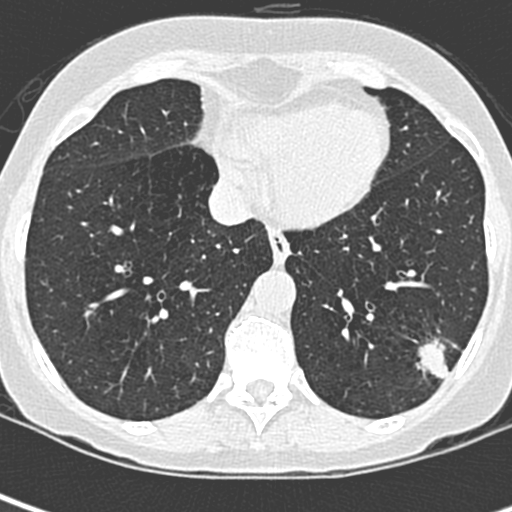
Low-dose screening chest CT, one axial slice; position 91 of 252 along the scan axis; lung window (W 1500 / L -600 HU); 1.3 mm slice thickness; 512 × 512 image matrix, field of view 271 × 271 mm.
Annotated regions visible in this slice (expert manual segmentation):
- lesion 1 (tumor, lower lobe of left lung): box from (x=418, y=339) to (x=448, y=381) px